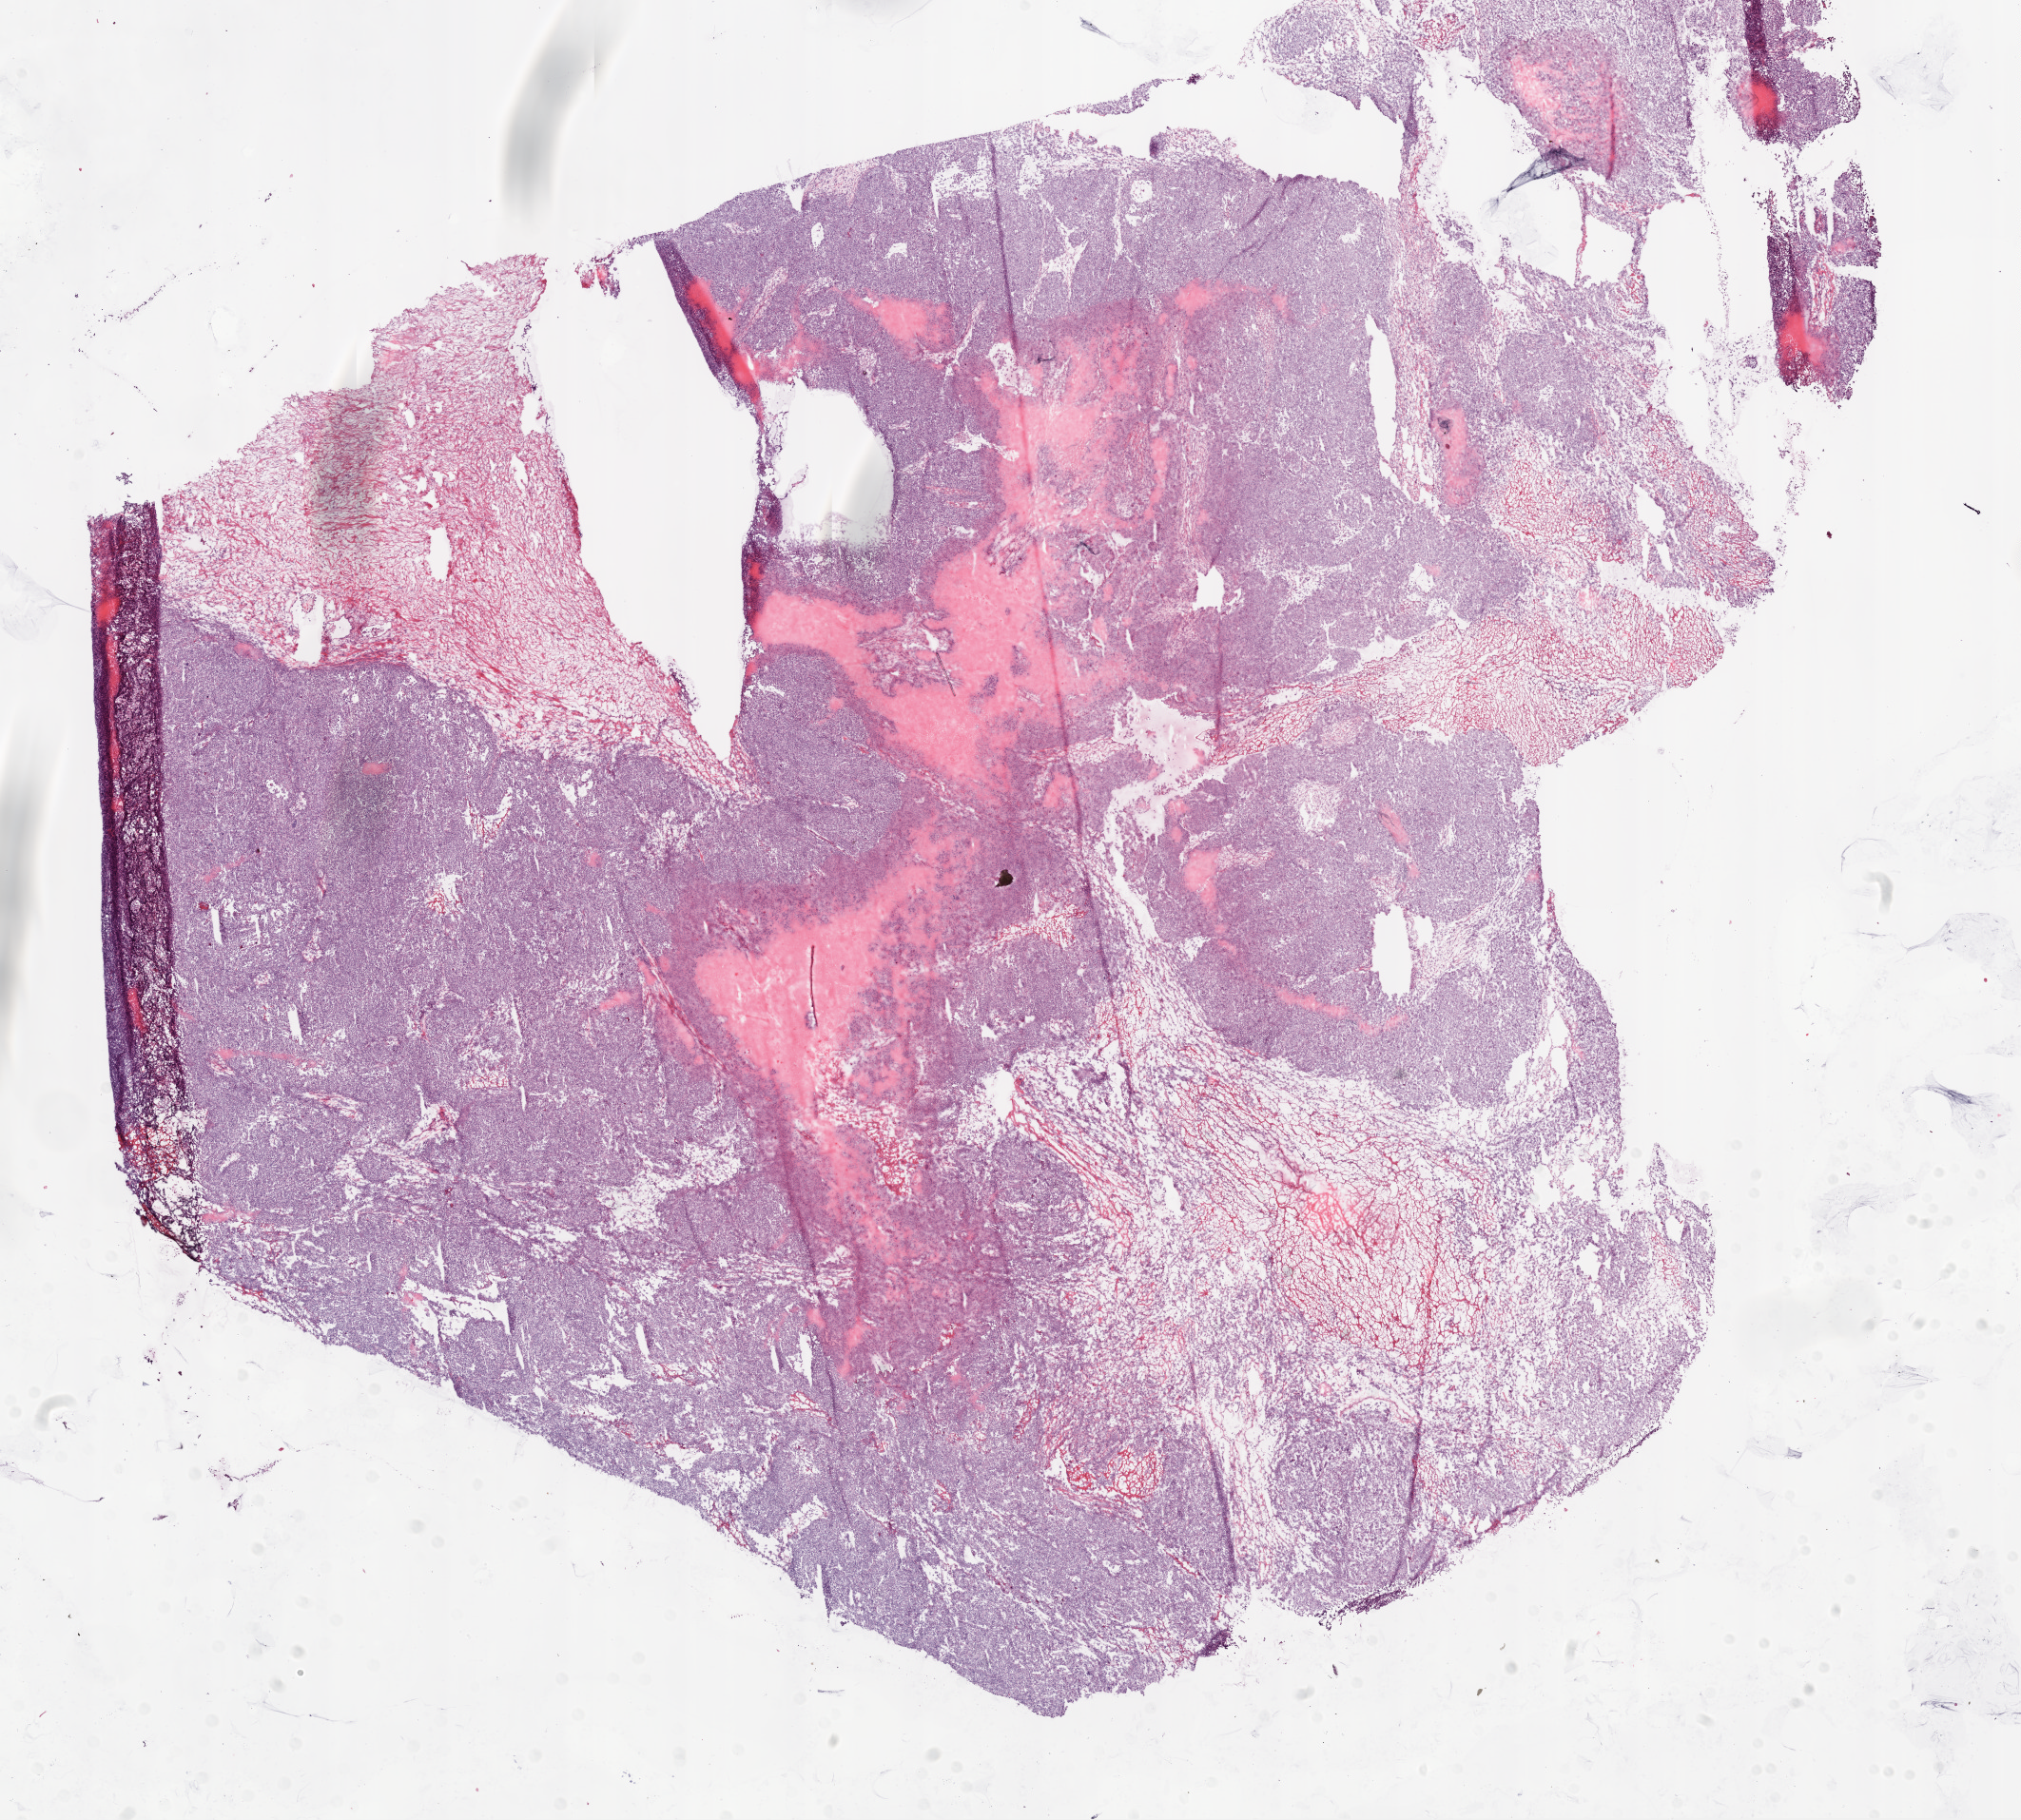
Whole-slide histology image, Hematoxylin and eosin (H&E) stained — low-resolution overview of the scanned area, about 17.1 x 15.4 mm (acquisition: 20x scan); frozen section from the bottom of the tissue portion; ovary, primary tumour sample. Female, age 63 years at initial diagnosis. Histologic grade: G3 (poorly differentiated). Slide review estimates, as recorded: tumour cells 80%, tumour nuclei 99%, normal cells 0%, stromal cells 18%, necrosis 2%.
FIGO stage: IIIC. Laterality: bilateral. Histologic diagnosis: Serous cystadenocarcinoma, NOS.